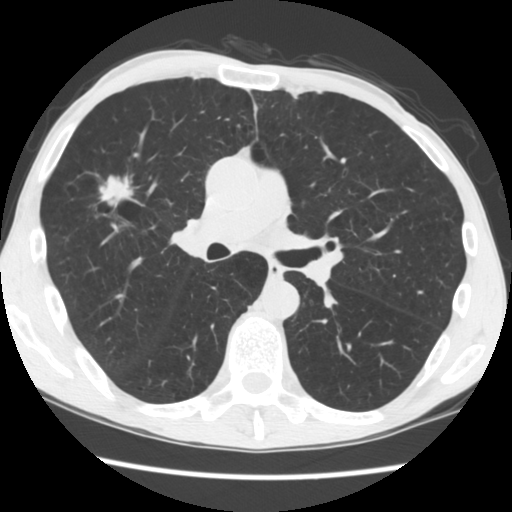
Axial slice from a low-dose chest CT screening exam. Second screening round (one year after baseline). Lung window (W 1500 / L -600 HU). 2.5 mm slice thickness. Standard (soft-tissue) reconstruction kernel (STANDARD). 512 × 512 image matrix. Male participant, aged 56 years at enrolment. Current smoker at enrolment.
- Expert-annotated lung lesion, bounding box [x1, y1, x2, y2] px = [89, 168, 147, 231].
- The screening reader recorded 2 non-calcified nodules or masses ≥4 mm on this exam (right upper lobe, left upper lobe); which of them this box marks is not recorded.
- Official screen result: positive, change unspecified: nodule(s) >= 4 mm or enlarging nodule(s), mass(es), or other non-specific abnormalities suspicious for lung cancer.
- Later outcome: lung cancer diagnosed 101 days after this screen — squamous cell carcinoma, NOS, right upper lobe, right middle lobe, well differentiated (G1), stage IA (AJCC 6th edition), 27 mm at pathology.